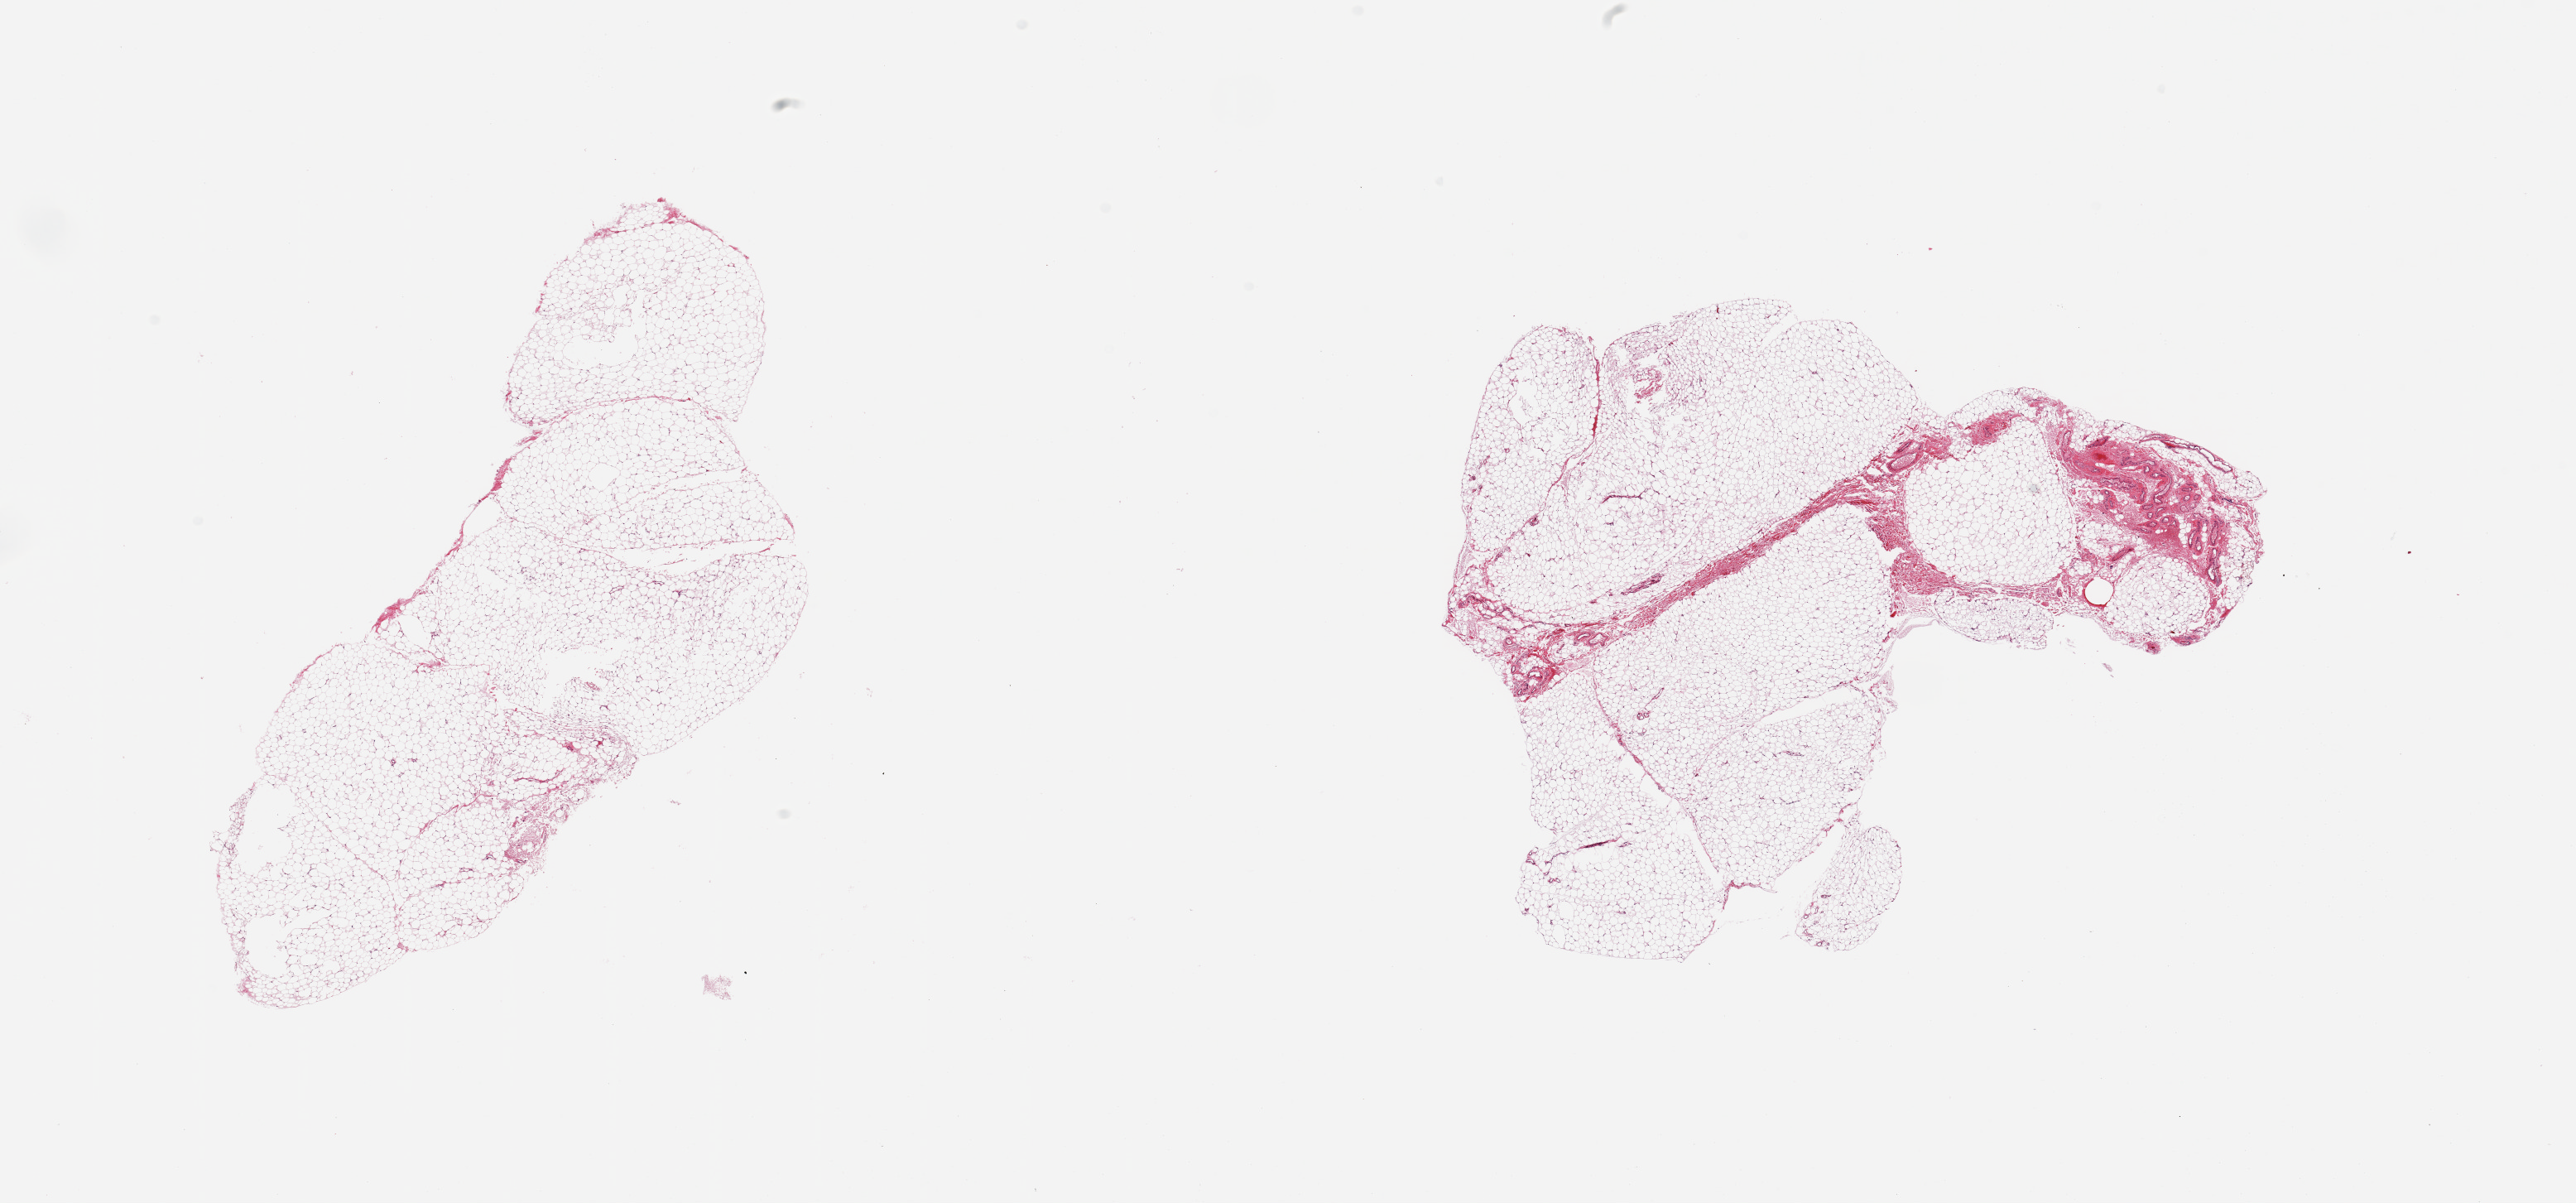
Haematoxylin and eosin whole-slide image — shown as a low-resolution overview of the whole scanned area (about 24.6 x 11.5 mm), PAXgene-fixed paraffin-embedded (PFPE) section, sampled site (target tissue): omentum, tissue donor sample. Donor sex: male.
- pathologist's review note for this sample: 2 pieces, ~5-10% fascia/vascular elements